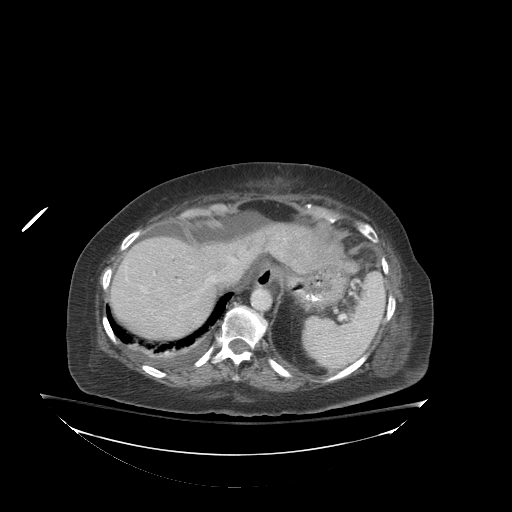
Contrast-enhanced abdominal CT (liver protocol), one axial slice. Slice 66 of 81 in the series (ordered by position). Reconstruction kernel STANDARD. 140 kVp. Soft-tissue window (W 400 / L 40 HU). 2.5 mm slice thickness. 512 × 512 image matrix, field of view 500 × 500 mm. From the clinical record (not read from this slice): diagnosis: hepatocellular carcinoma (patient treated with transarterial chemoembolisation; whether this scan precedes or follows treatment is not stated here); TNM stage (as recorded): Stage-I; Child-Pugh class: B; tumour nodularity: uninodular.
Structures marked on this image (semi-automatic segmentation, software-assisted and operator-edited):
- liver parenchyma outside the tumour (the mass and vessels are separate outlines, so this box may not span the whole liver): bounding box [x1, y1, x2, y2] px = [110, 226, 276, 340]
- liver vessels: [126, 259, 234, 293]